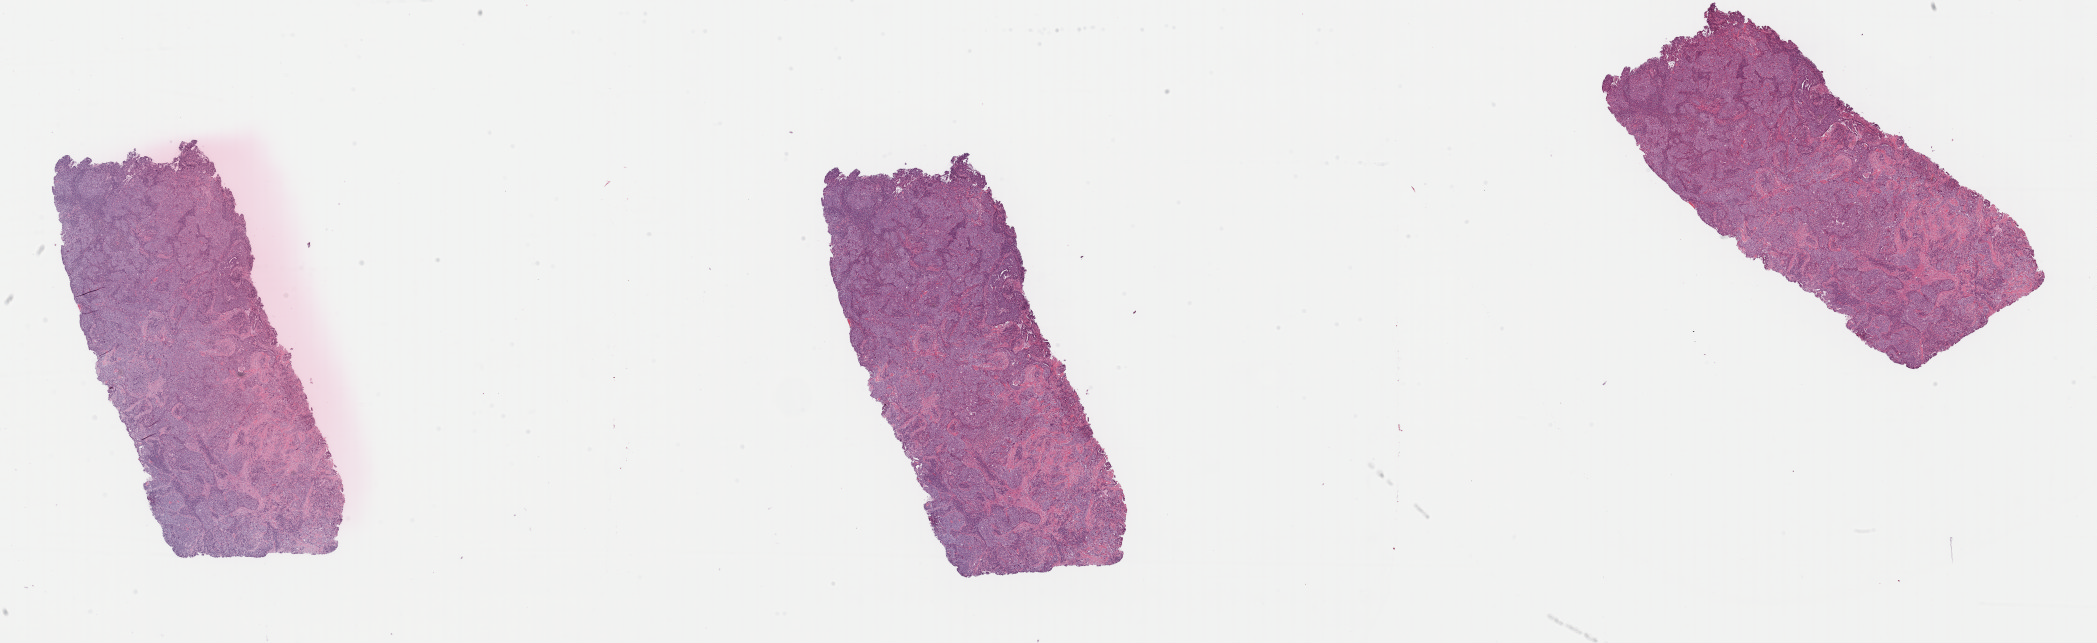
Whole-slide histology image, H&E, a low-resolution overview of the entire scanned area, about 33.1 x 10.2 mm (acquisition: 40x scan). Formalin-fixed paraffin-embedded (FFPE) diagnostic section. Primary tumour sample from the breast. Female, age 52 years at initial diagnosis.
Pathologic diagnosis: Infiltrating duct carcinoma, NOS. AJCC pathologic stage: IIA (7th edition). Lymph nodes positive (case pathology): 0 of 6 examined.